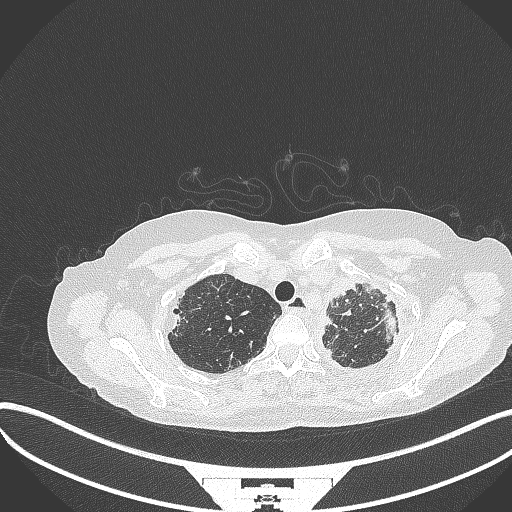
Chest CT, one axial slice. Slice 292 of 373 in the series (ordered by position). Reconstruction kernel B70f. 120 kVp. Lung window (W 1500 / L -600 HU). 512 × 512 image matrix, field of view 400 × 400 mm. Female patient, age 56 years. From the clinical record (not read from this slice): clinical TNM (as recorded): T1 N0 M0.
Annotated regions visible in this slice (bounding box drawn by a radiologist):
- lung tumour (recorded histology: adenocarcinoma): bounding box <383,302,406,350> (left, top, right, bottom; pixels)